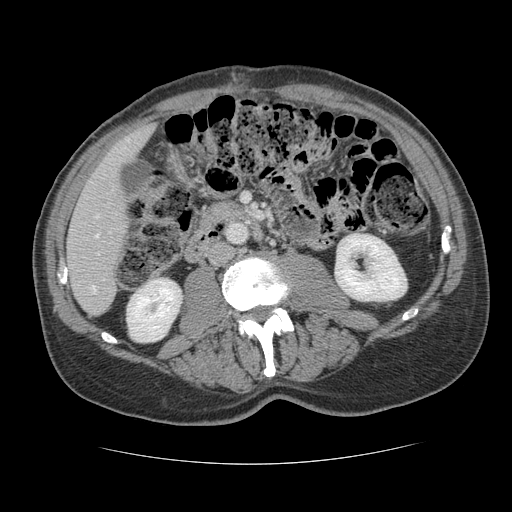
Contrast-enhanced abdominal CT, one axial slice. Position 41 of 134 along the scan axis. 120 kVp. Intravenous contrast given. Soft-tissue window (W 400 / L 40 HU). 2.5 mm slice thickness. 512 × 512 image matrix. Male patient, age 68 years. From the clinical record (not read from this slice): diagnosis: colorectal cancer liver metastases, imaged before liver resection; multiple liver metastases: yes; largest metastasis: 2.2 cm.
Annotated regions visible in this slice (outlined manually by an expert reader):
- hepatic veins: box from (x=95, y=216) to (x=99, y=238) px
- liver: (x=67, y=127)–(x=151, y=315)
- planned liver remnant (the part of the liver to remain after resection): (x=67, y=127)–(x=151, y=315)
- portal vein (with intrahepatic branches): (x=92, y=253)–(x=99, y=292)